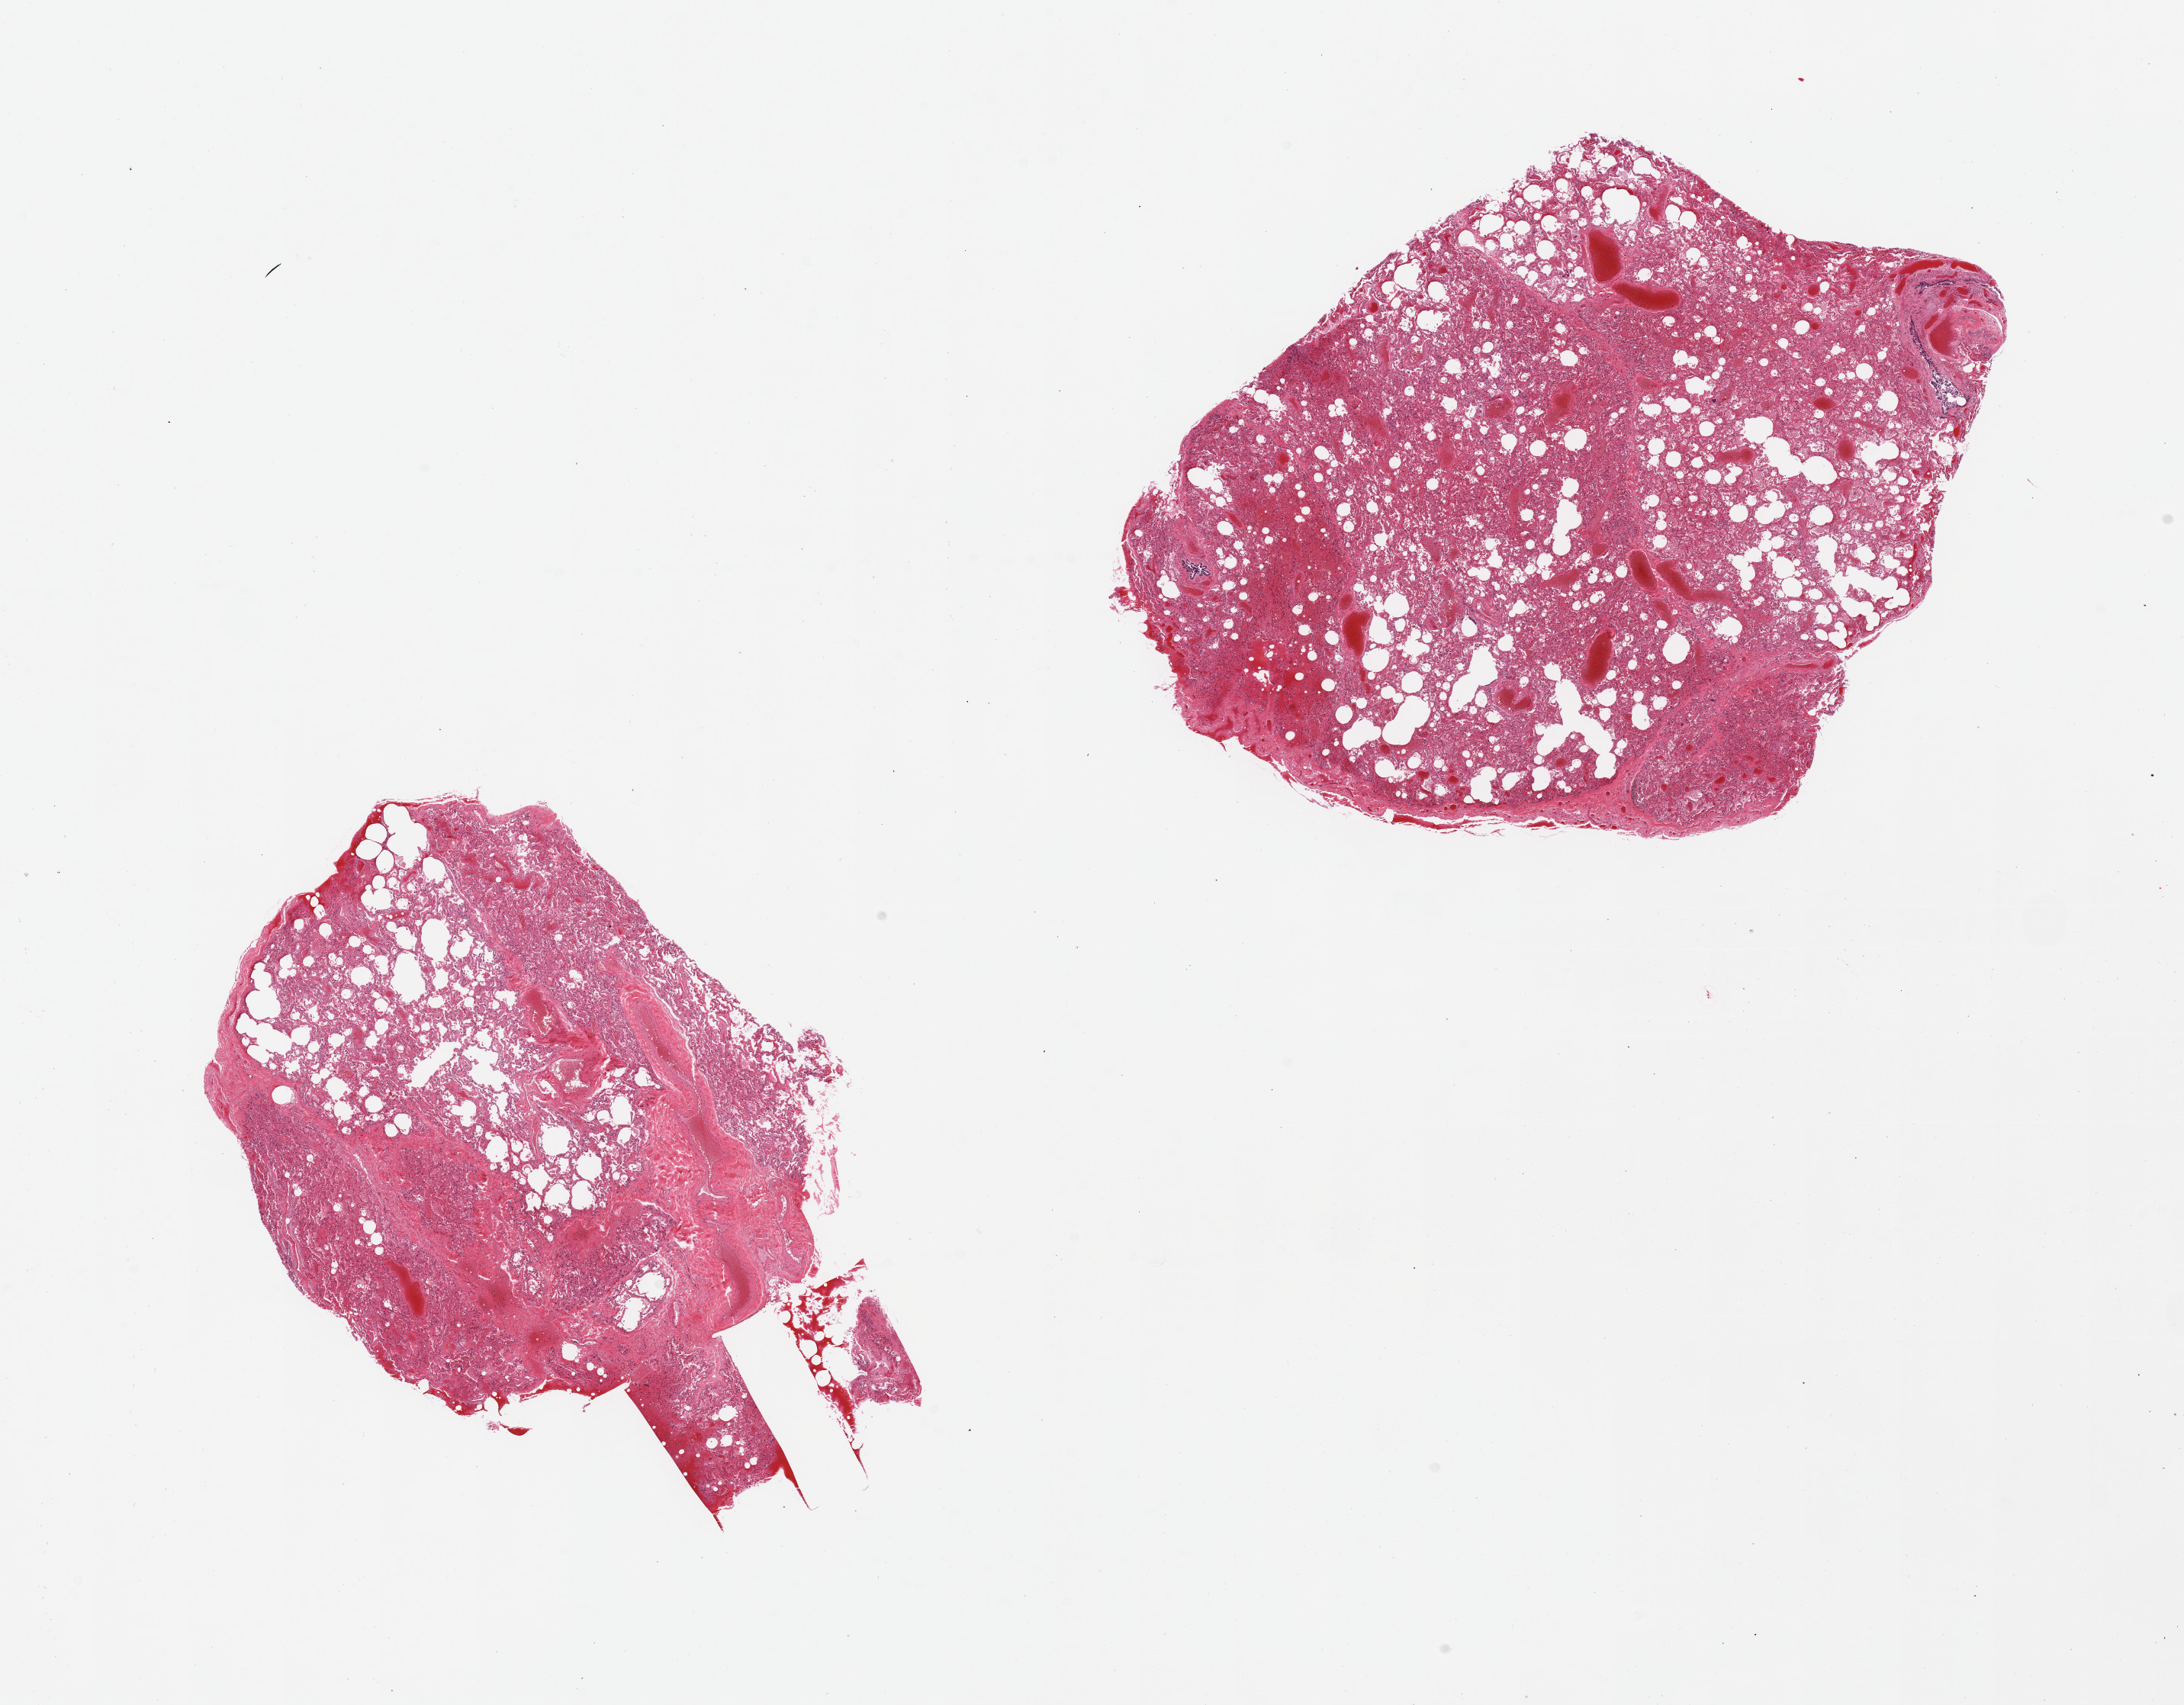
Haematoxylin and eosin whole-slide image, low-resolution overview of the scanned area, about 22.6 x 17.7 mm, PAXgene-fixed, paraffin-embedded tissue, target tissue: lung, tissue donor sample. Donor: male.
Reviewer comment on this tissue sample: 2 pieces. Moderate congestion.